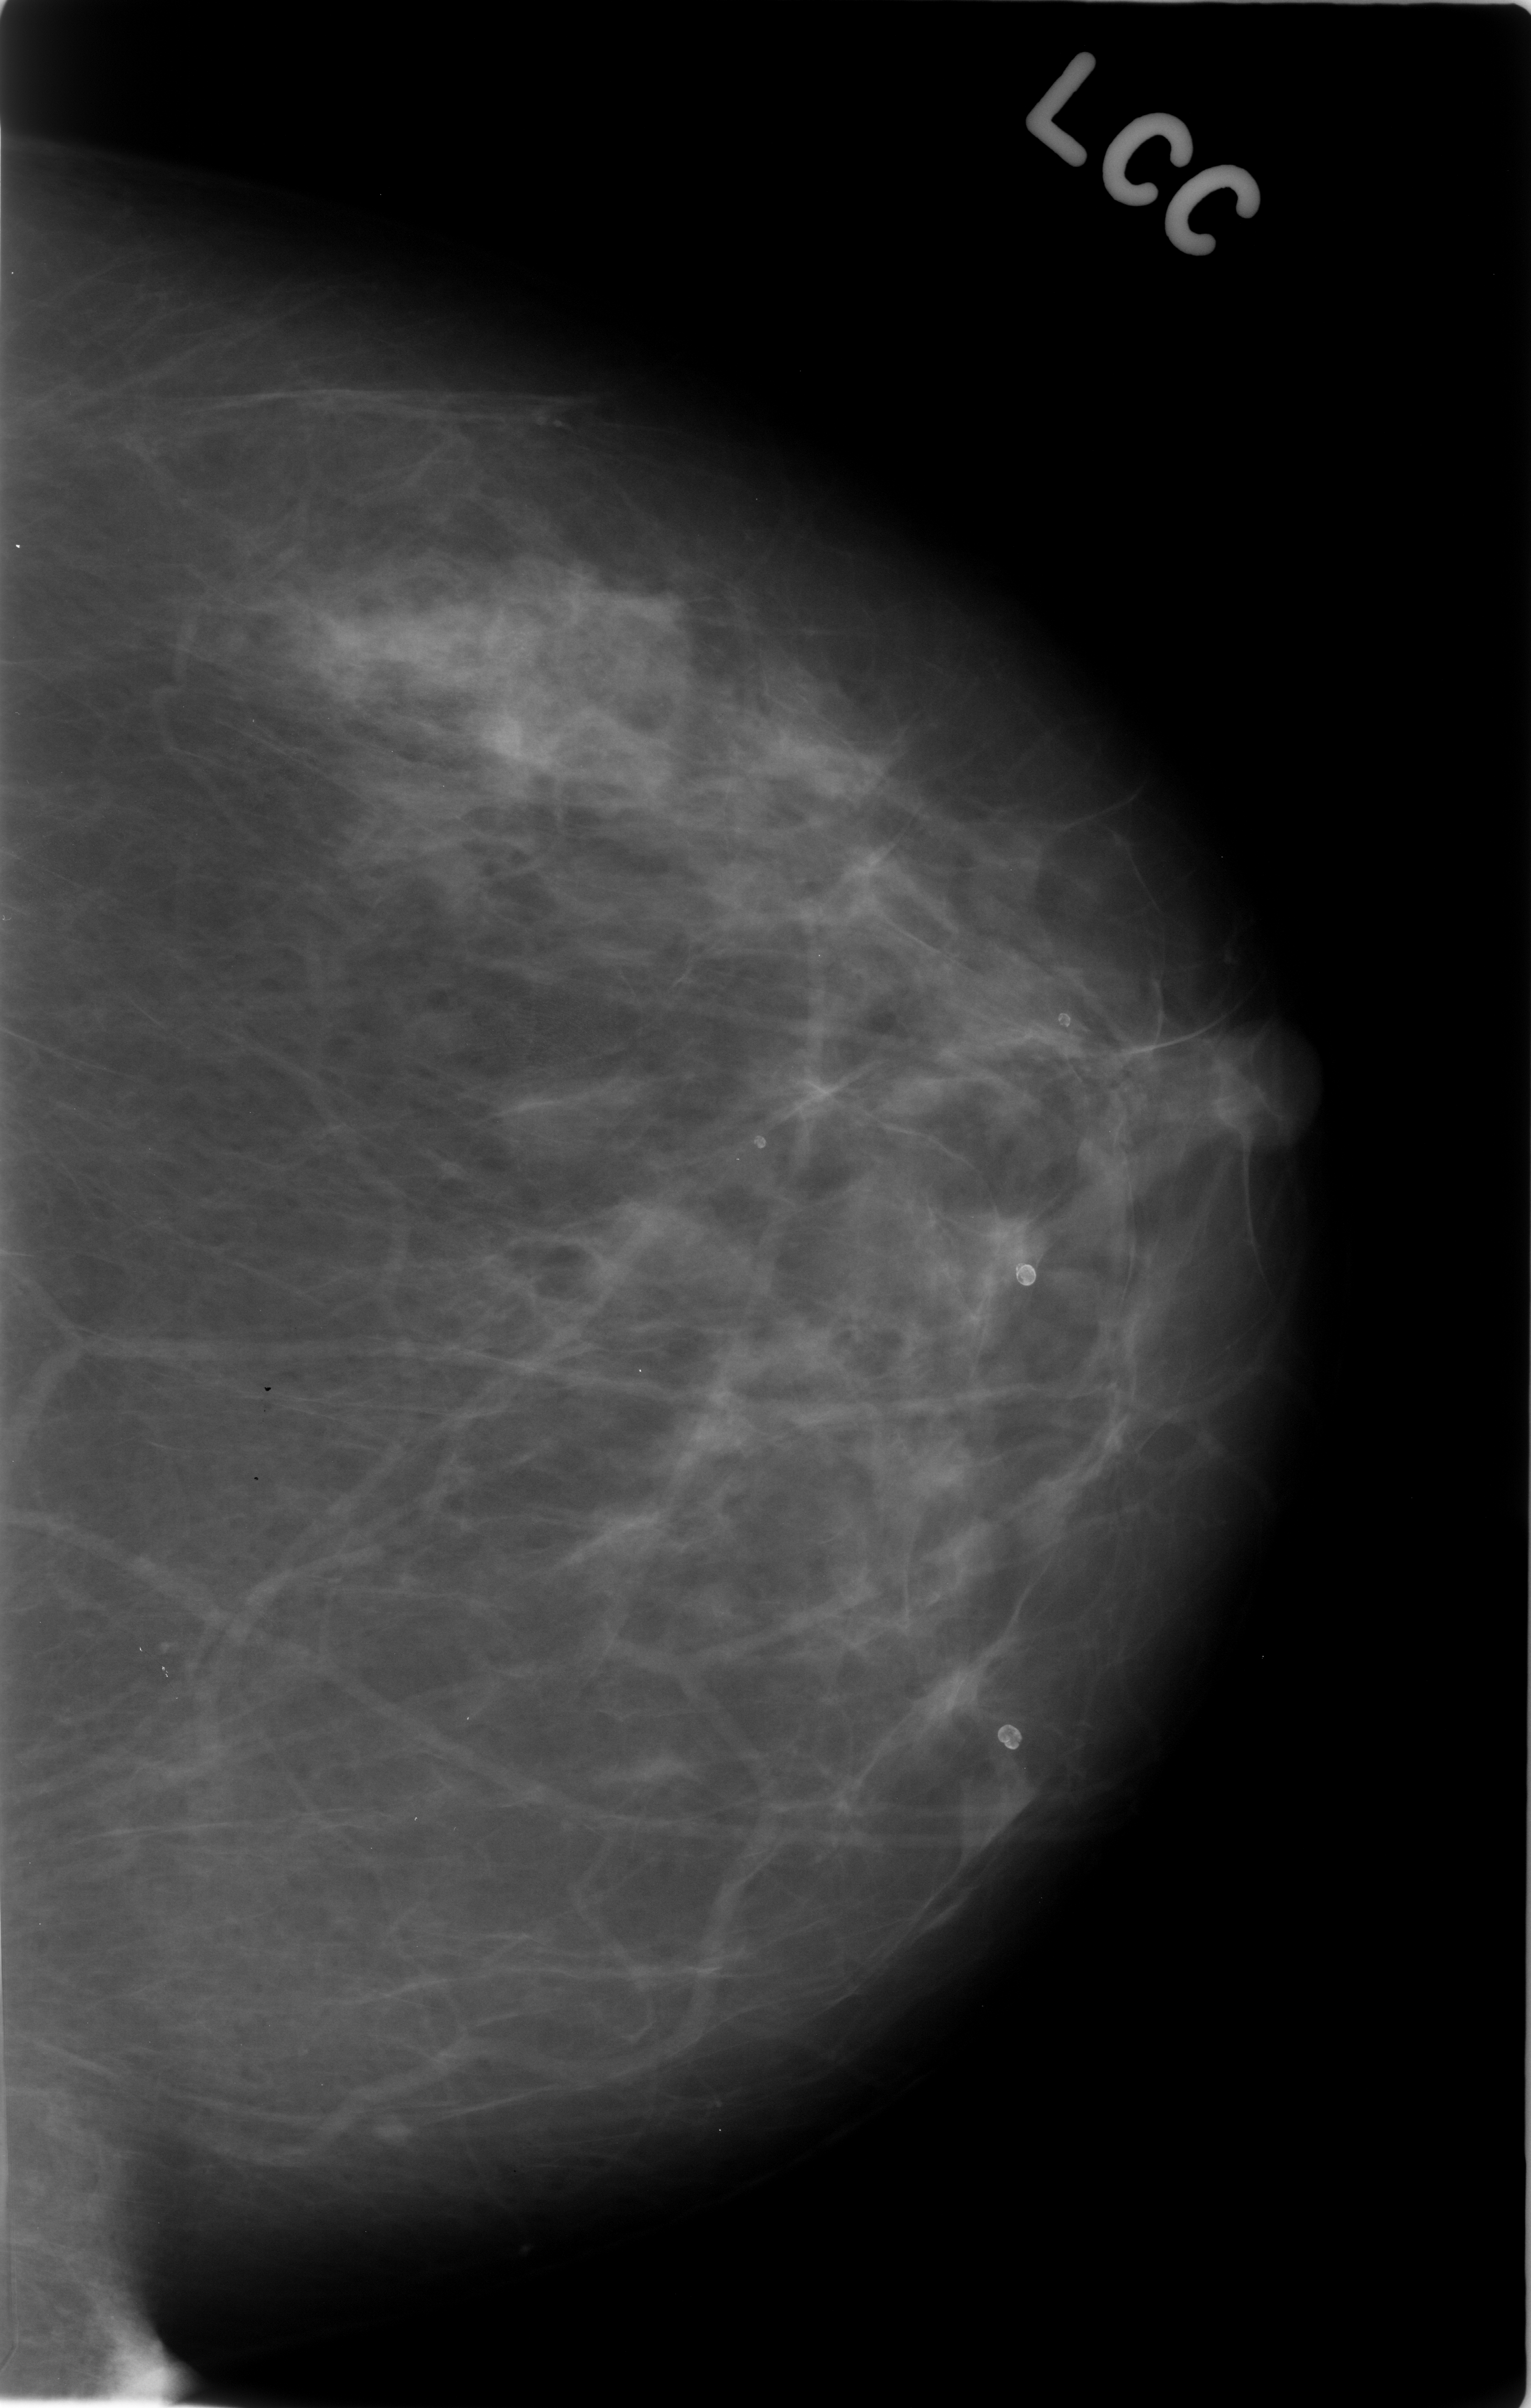
Digitized screen-film mammogram. Left breast. Craniocaudal (CC) view. Breast composition: scattered fibroglandular densities (BI-RADS density category 2 of 4). 1531 × 2408 image matrix.
Expert-marked regions of interest on this image (one box per marked abnormality):
- calcifications, morphology amorphous, distribution clustered; BI-RADS assessment category 4; subtlety rating 1 on a 1 (subtle) to 5 (obvious) scale; pathology result (as recorded, not read from the image): benign: bounding box [x1, y1, x2, y2] px = [453, 578, 601, 739]